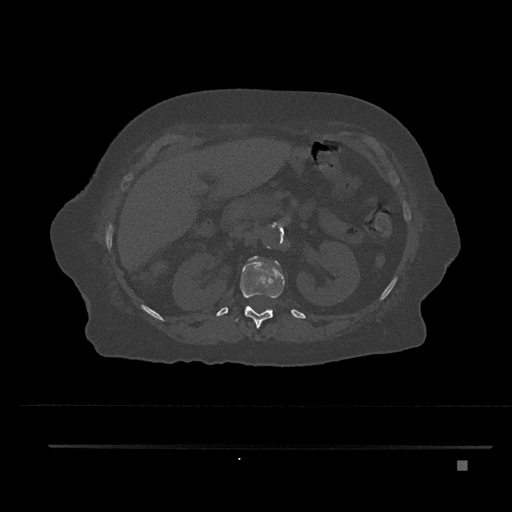
CT including the spine, one axial slice. Position 255 of 797 along the scan axis. Reconstruction kernel Br40s/3. 120 kVp. Bone window (W 1800 / L 400 HU). 0.5 mm slice thickness. 512 × 512 image matrix. Female patient, age 76 years. Case-level facts recorded for this patient, not image findings: primary cancer: lung; vertebrae with lytic lesions (as recorded): T11, L3.
Annotated regions visible in this slice (semi-automatic segmentation, software-assisted and operator-edited):
- L1 vertebra: bounding box (x1, y1, x2, y2) in pixels: (249, 257, 279, 264)
- T12 vertebra: (235, 261, 284, 329)